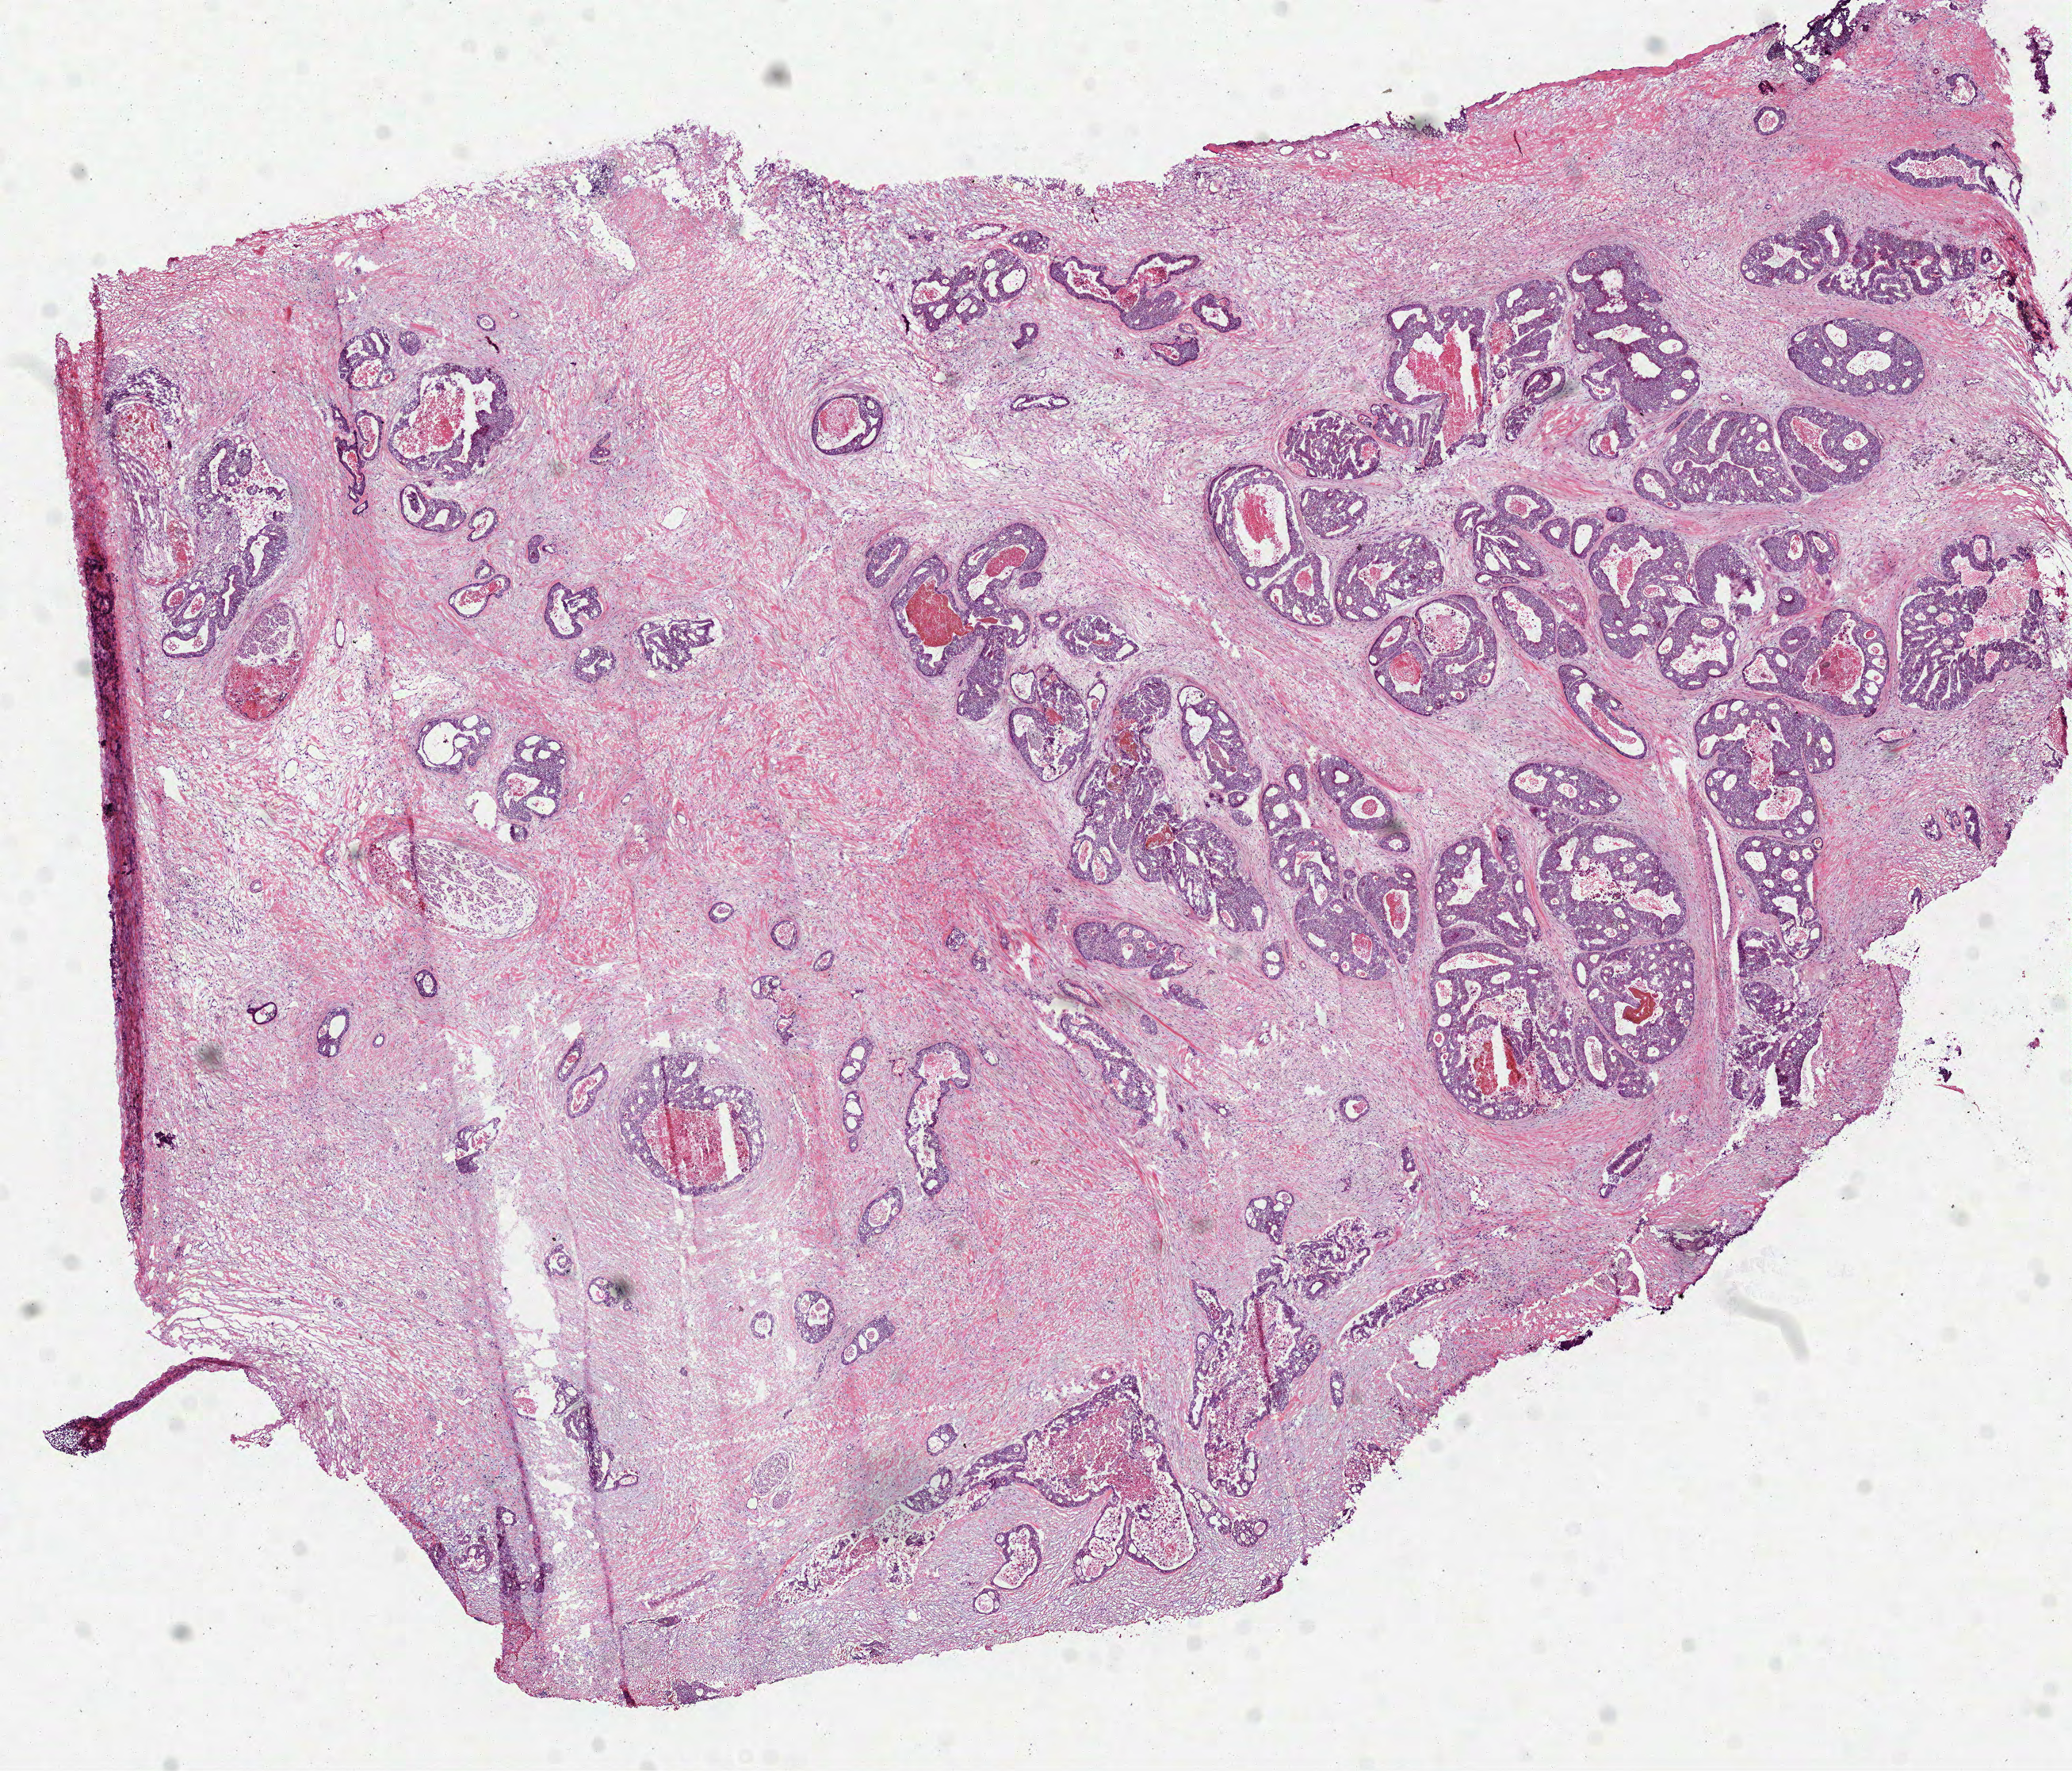
Digitized H&E-stained tissue section (whole slide) — shown as a low-resolution overview of the whole scanned area (about 10.5 x 9.0 mm, acquisition: 40x scan), frozen section, sample: primary tumour, rectum. Male patient; age at initial diagnosis 56 years. Slide review estimates, as recorded: tumour cells 60%, tumour nuclei 80%, normal cells 0%, stromal cells 30%, necrosis 10%.
• diagnosis: Adenocarcinoma, NOS (rectosigmoid junction)